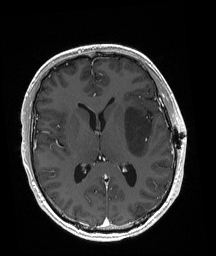
Brain MRI from a brain-tumour surgery series, one axial slice. Position 95 of 192 along the scan axis. T1-weighted post-contrast. 1 mm slice thickness. 216 × 256 image matrix, field of view 211 × 250 mm. Case-level facts recorded for this patient, not image findings: histopathology: Astrocytoma; WHO grade: 3; IDH mutation: yes; tumour location: Left Posterior Frontal.
Annotated regions visible in this slice (expert manual segmentation):
- tumour: box from (x=124, y=108) to (x=152, y=157) px